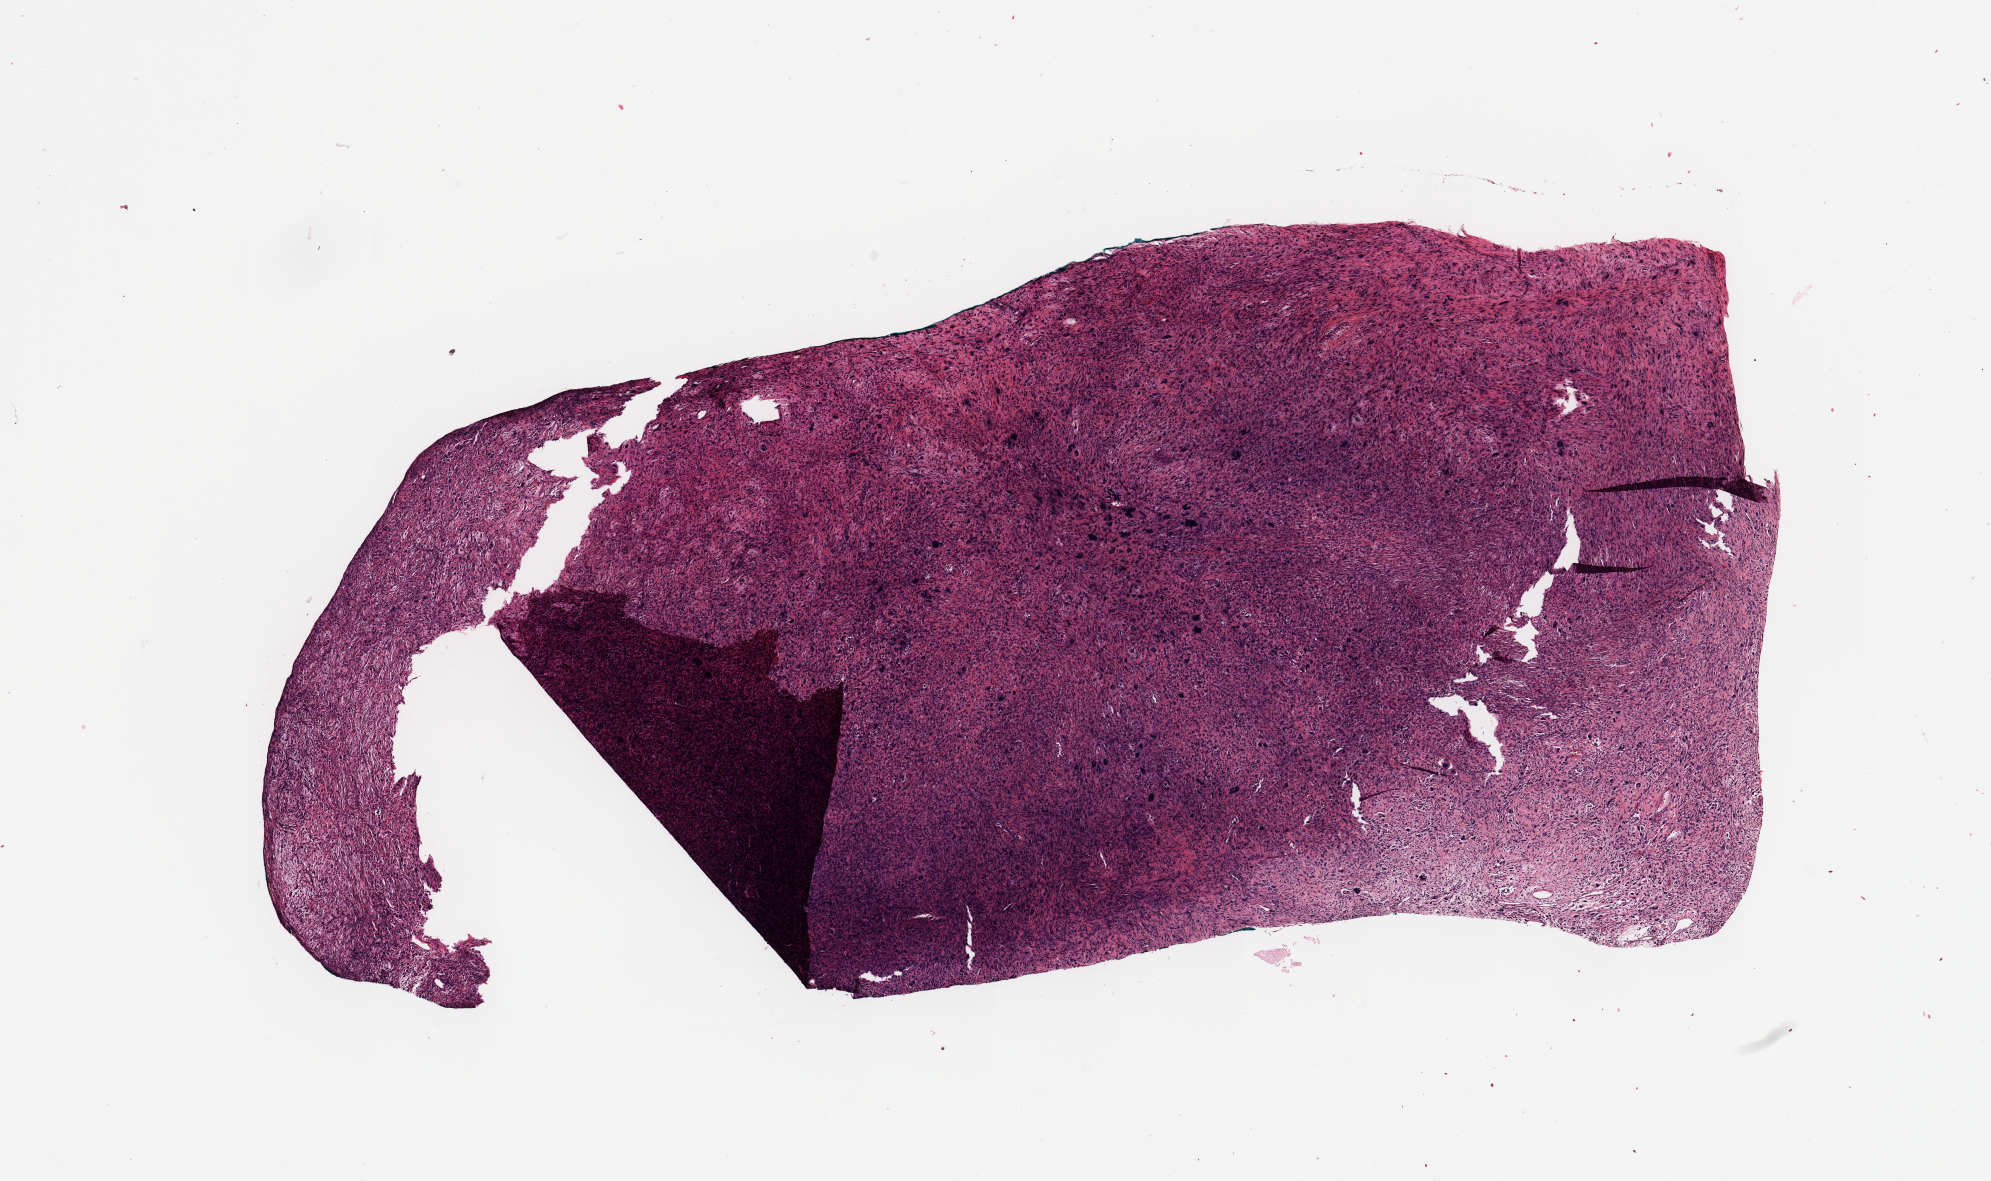
Whole-slide histology image, Hematoxylin and eosin (H&E) stained — whole scanned area (about 15.8 x 9.3 mm, slide scanned at 20x) shown as a low-resolution overview; tumour tissue sample. Patient: male, age 60 years.
- patient diagnosis (cohort enrolment): sarcoma (site not recorded at cohort level)
- primary tumour site (as recorded): lower extremity